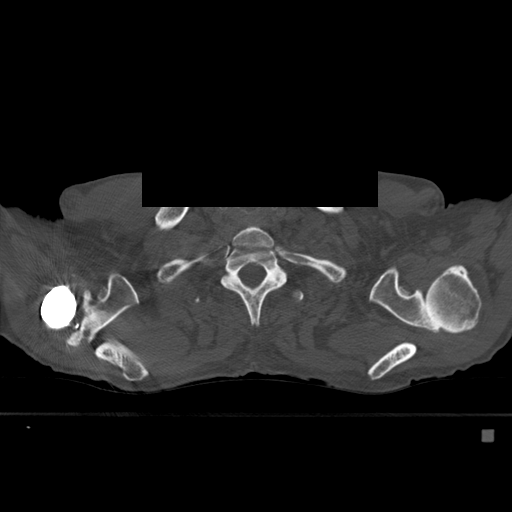
CT including the spine, one axial slice; slice 446 of 527 in the series (ordered by position); bone window (W 1800 / L 400 HU); 1.5 mm slice thickness; 512 × 512 image matrix. Male patient, age 78 years. From the clinical record (not read from this slice): primary cancer: prostate.
Annotated regions visible in this slice (semi-automatically segmented with operator editing):
- T1 vertebra: bounding box [x1, y1, x2, y2] px = [233, 227, 274, 247]
- T2 vertebra: [221, 240, 287, 325]
- T3 vertebra: [206, 290, 304, 305]